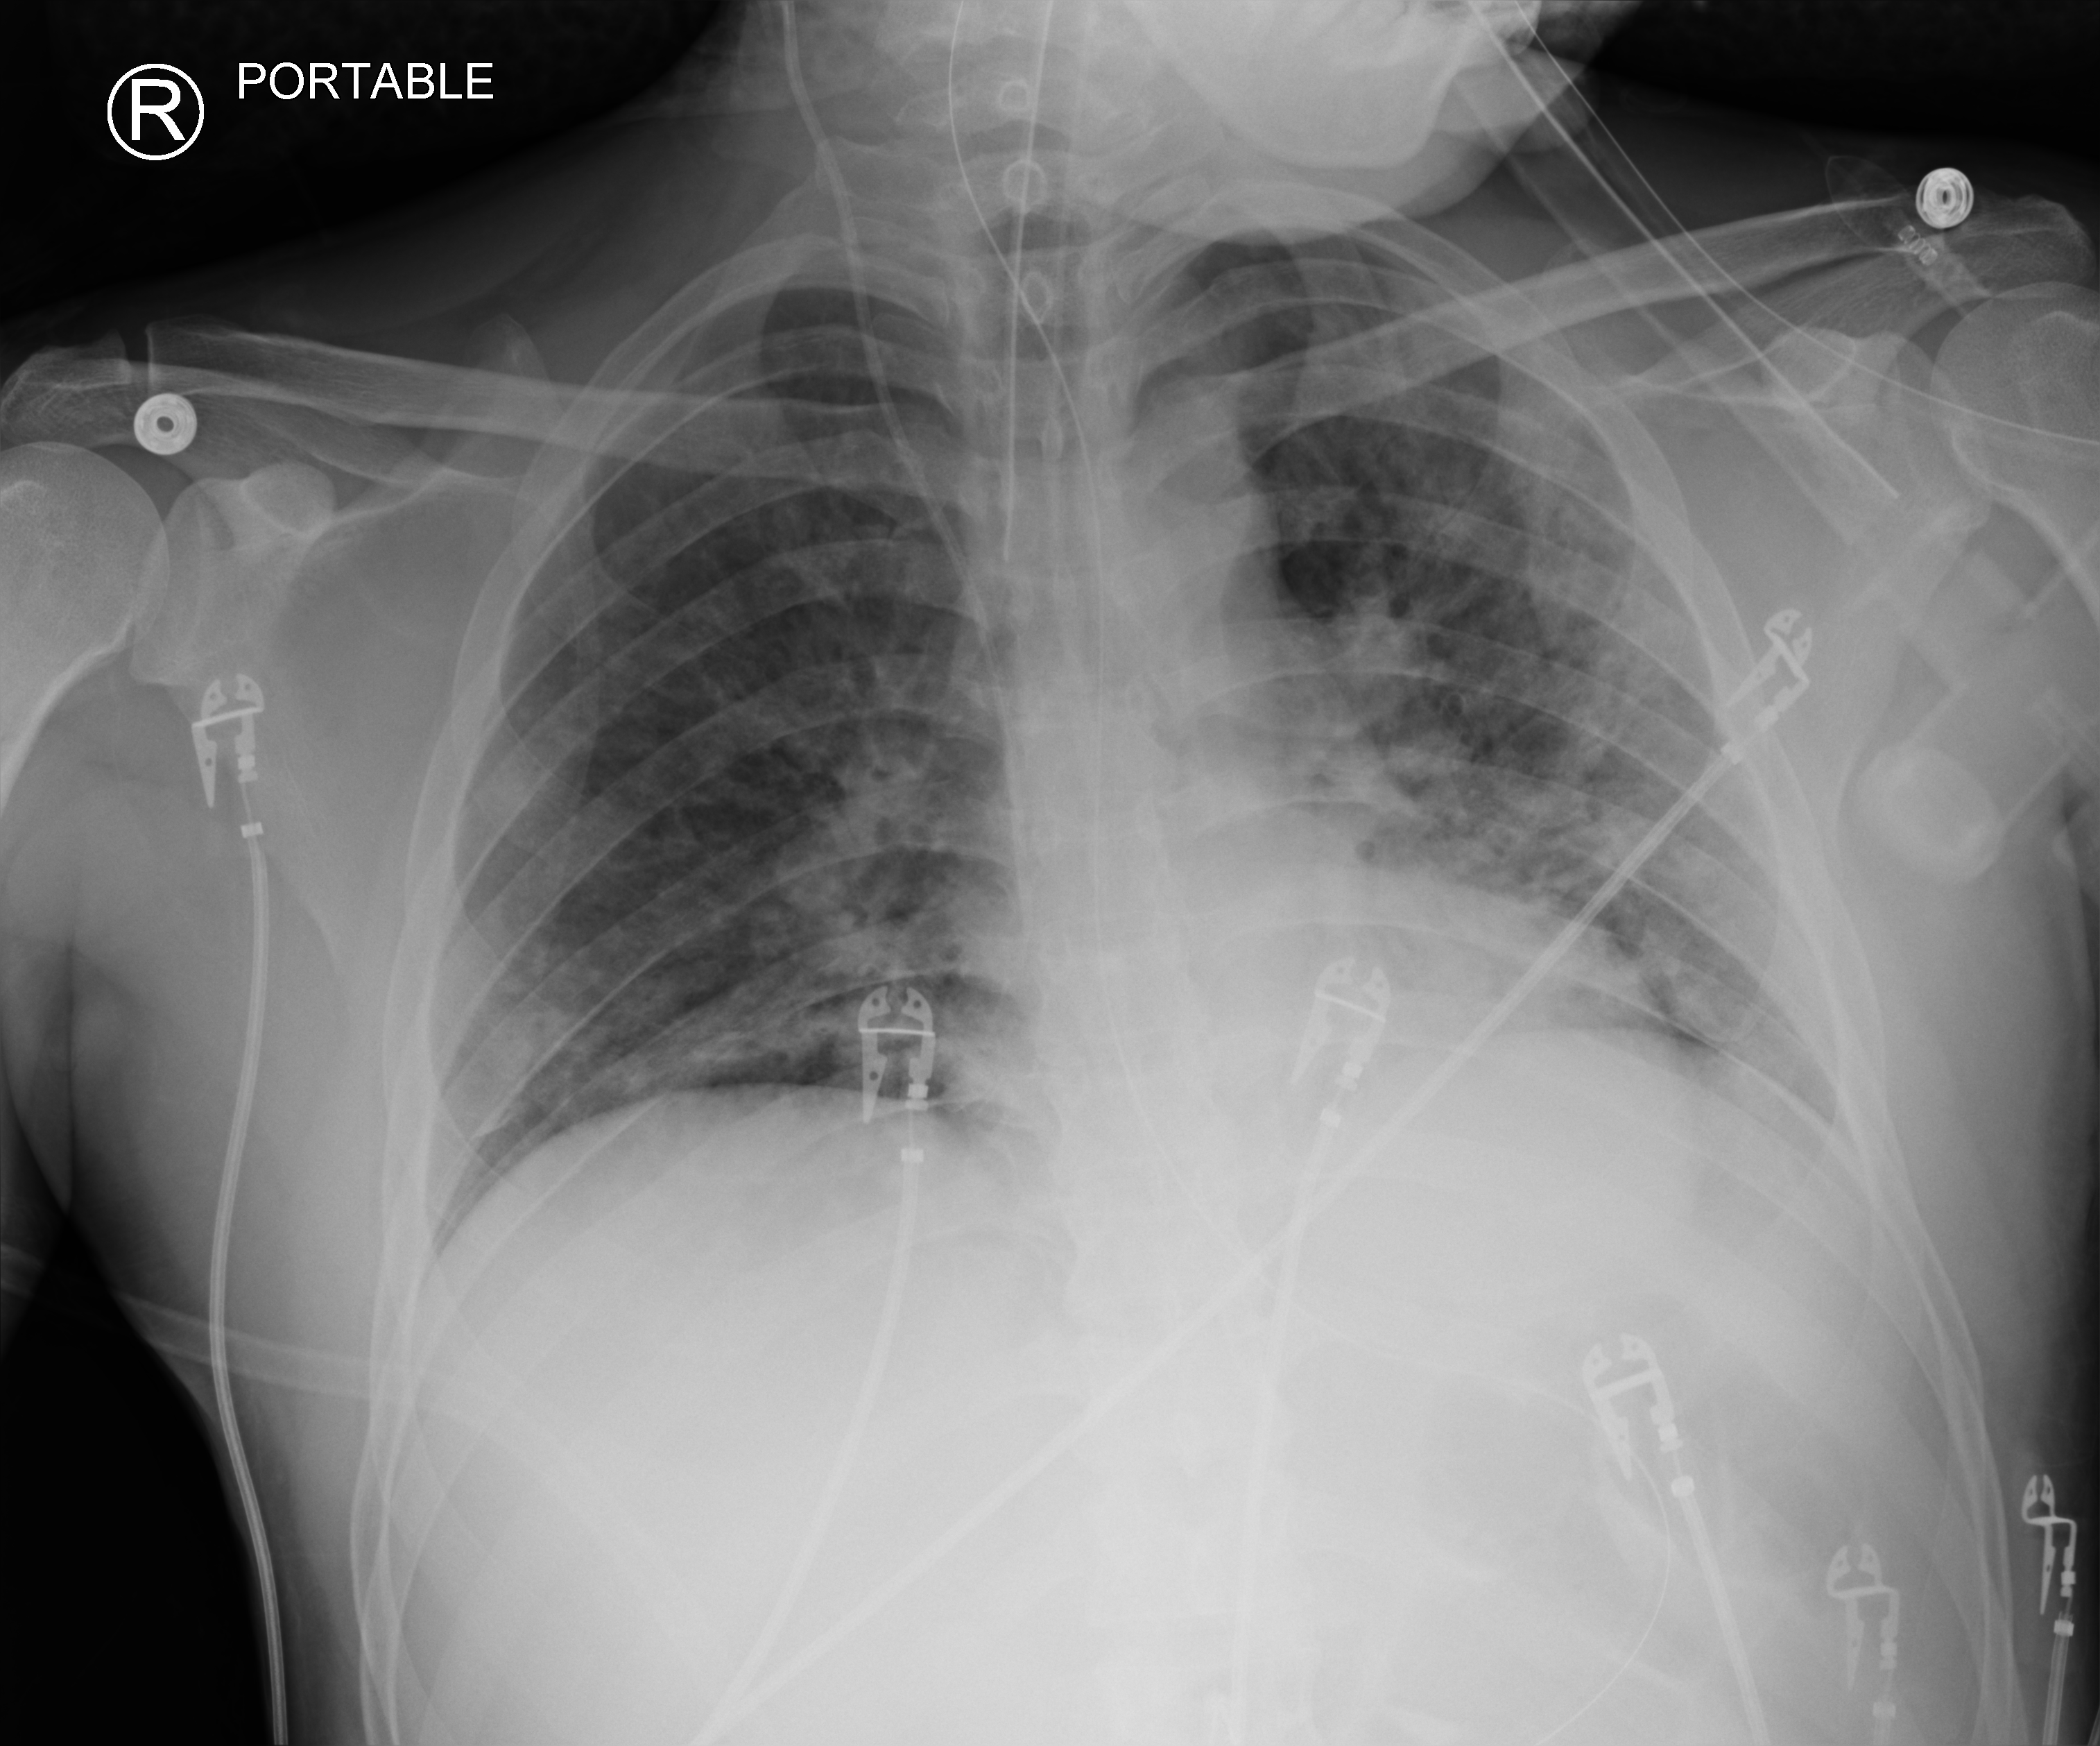
Portable chest radiograph. Patient hospitalised with COVID-19; male, aged 18–59 years.
Hospital-stay facts (about this admission, not read from this image; timing relative to this image not recorded):
- mechanically ventilated during this hospital stay: yes
- admitted to intensive care during this hospital stay: yes